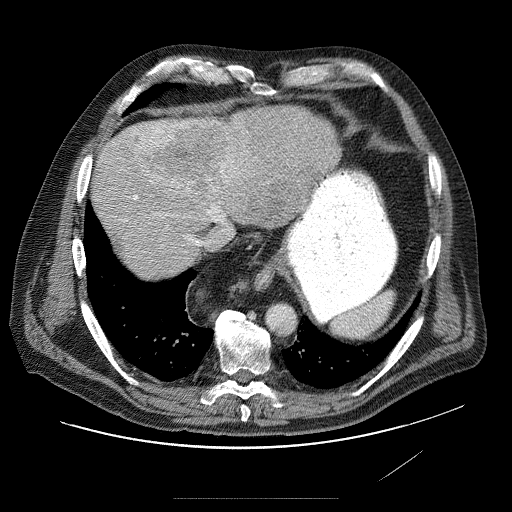
Contrast-enhanced abdominal CT (liver protocol), one axial slice. Slice 69 of 89 in the series (ordered by position). Reconstruction kernel STANDARD. Soft-tissue window (W 400 / L 40 HU). 512 × 512 image matrix, field of view 420 × 420 mm. From the clinical record (not read from this slice): diagnosis: hepatocellular carcinoma (patient treated with transarterial chemoembolisation; whether this scan precedes or follows treatment is not stated here); TNM stage (as recorded): Stage-IVA; Child-Pugh class: A.
Structures marked on this image (semi-automatic segmentation, software-assisted and operator-edited):
- liver parenchyma outside the tumour (the mass and vessels are separate outlines, so this box may not span the whole liver): bounding box [x1, y1, x2, y2] px = [92, 108, 340, 256]
- mass: [112, 117, 305, 221]
- liver vessels: [129, 167, 253, 239]